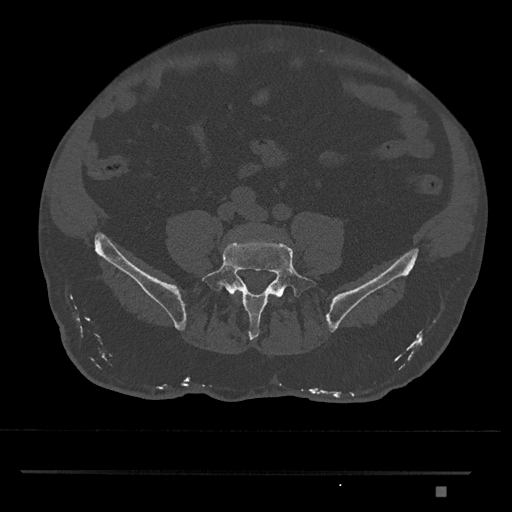
CT including the spine, one axial slice; slice 563 of 1134 in the series (ordered by position); 120 kVp; bone window (W 1800 / L 400 HU); 0.5 mm slice thickness; 512 × 512 image matrix, field of view 429 × 429 mm. Patient: male, 65 years. From the clinical record (not read from this slice): primary cancer: prostate.
Annotated regions visible in this slice (semi-automatic segmentation, software-assisted and operator-edited):
- L4 vertebra: bounding box (x1, y1, x2, y2) in pixels: (231, 291, 238, 297)
- L5 vertebra: (201, 241, 317, 340)